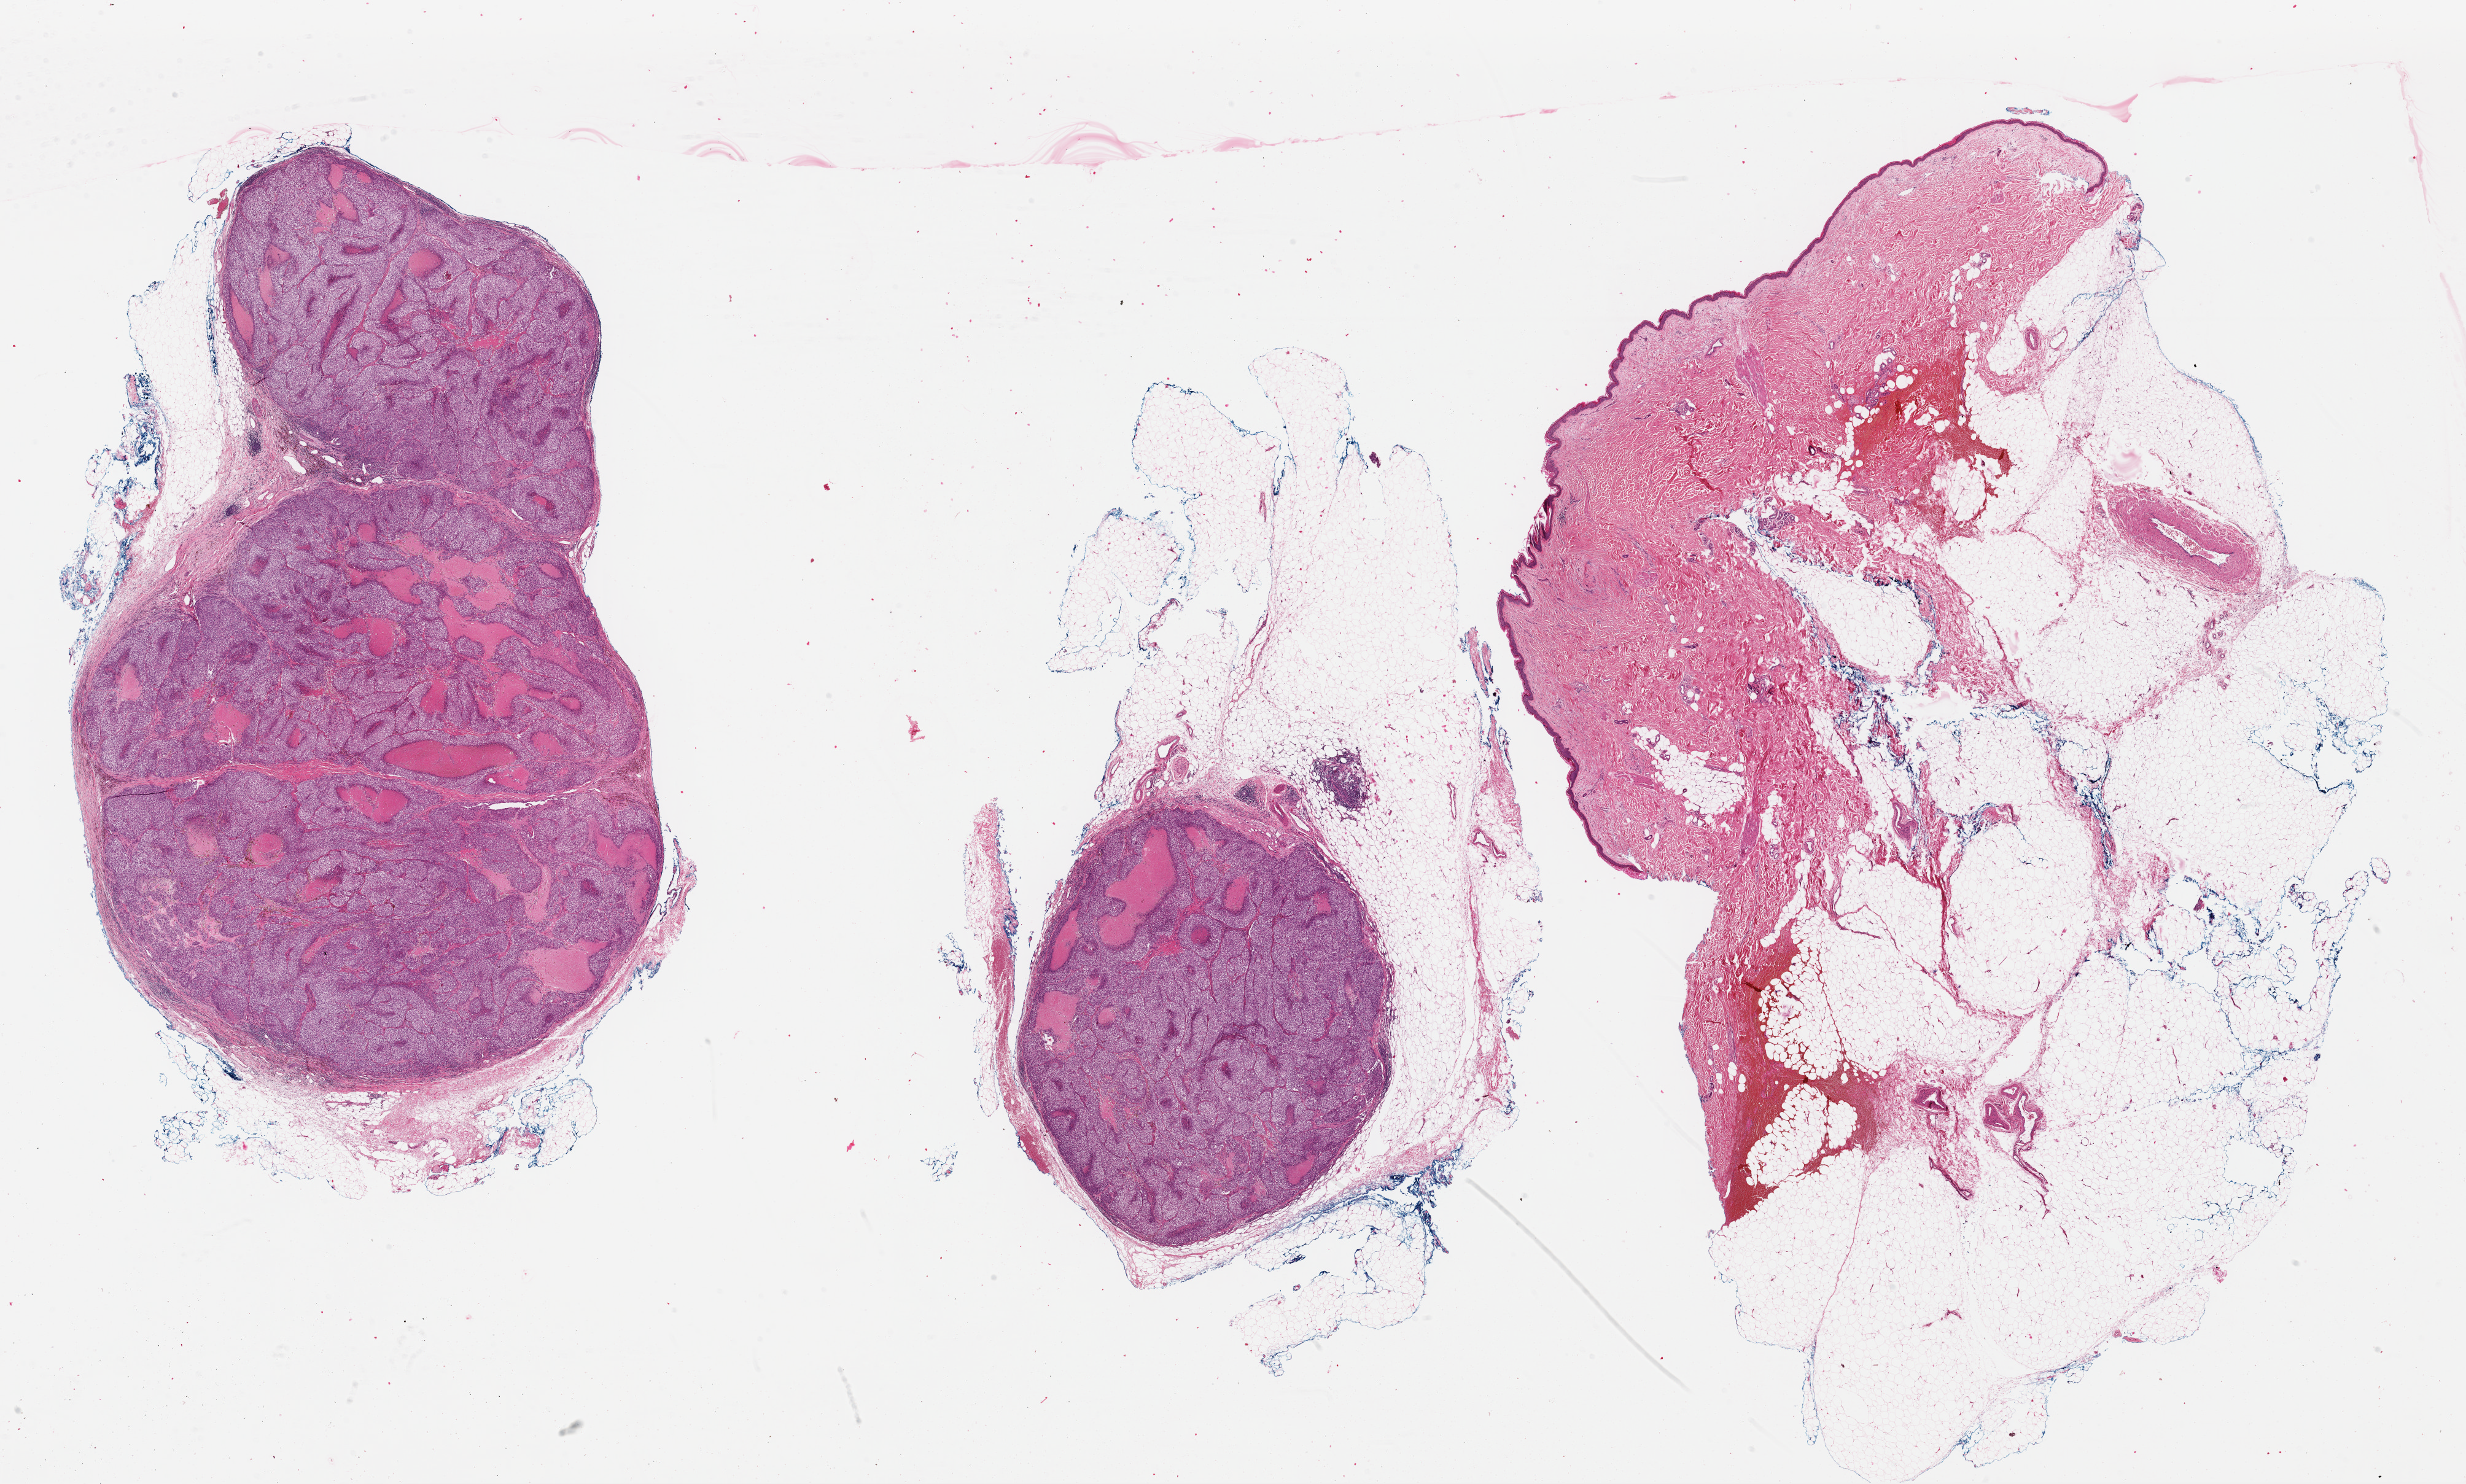
H&E-stained whole-slide image — whole scanned area (about 31.6 x 19.0 mm, slide scanned at 40x) shown as a low-resolution overview. Formalin-fixed paraffin-embedded (FFPE) diagnostic section. Skin, primary tumour sample. Male, age 79 years at initial diagnosis.
Diagnosis: Malignant melanoma, NOS.